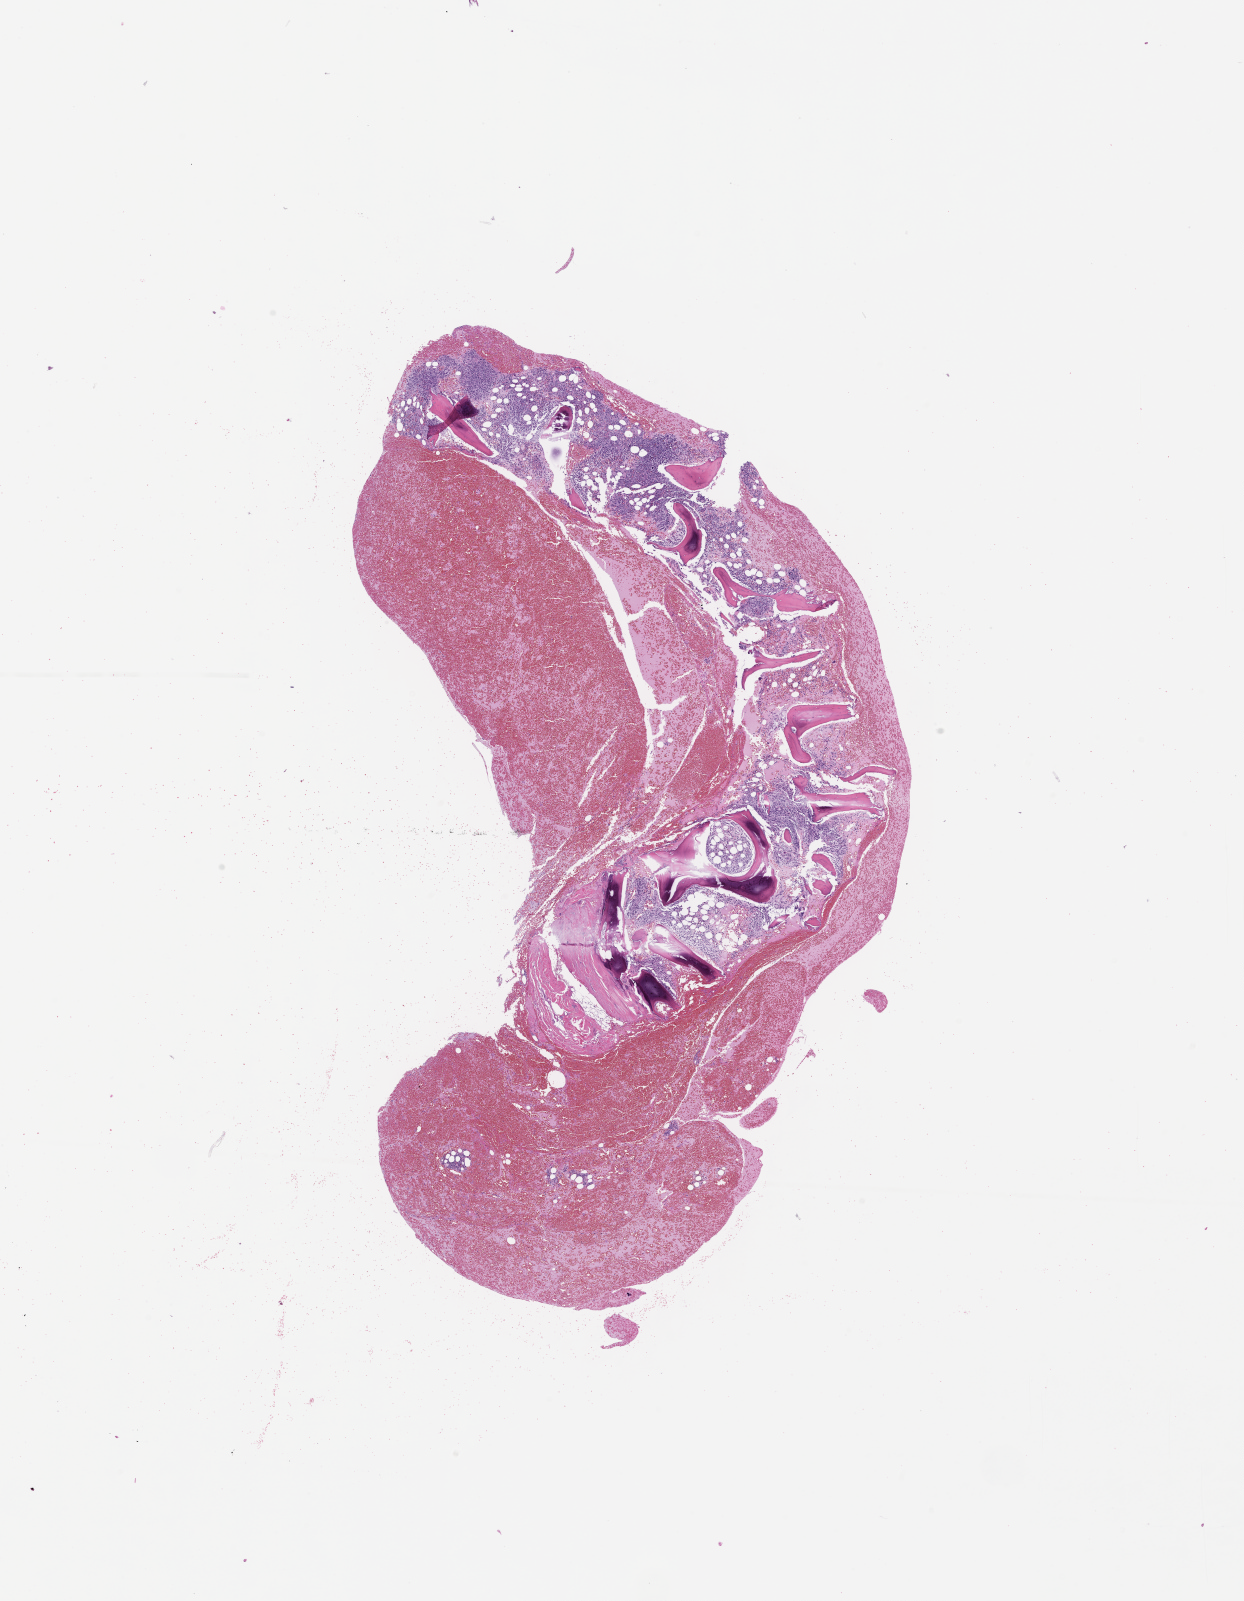
Whole-slide image, H&E stain — whole scanned area (about 10.1 x 12.9 mm) shown as a low-resolution overview, formalin-fixed, paraffin-embedded (FFPE) tissue, site: bone marrow. Patient: female.
From a patient with: Plasma Cell Myeloma.